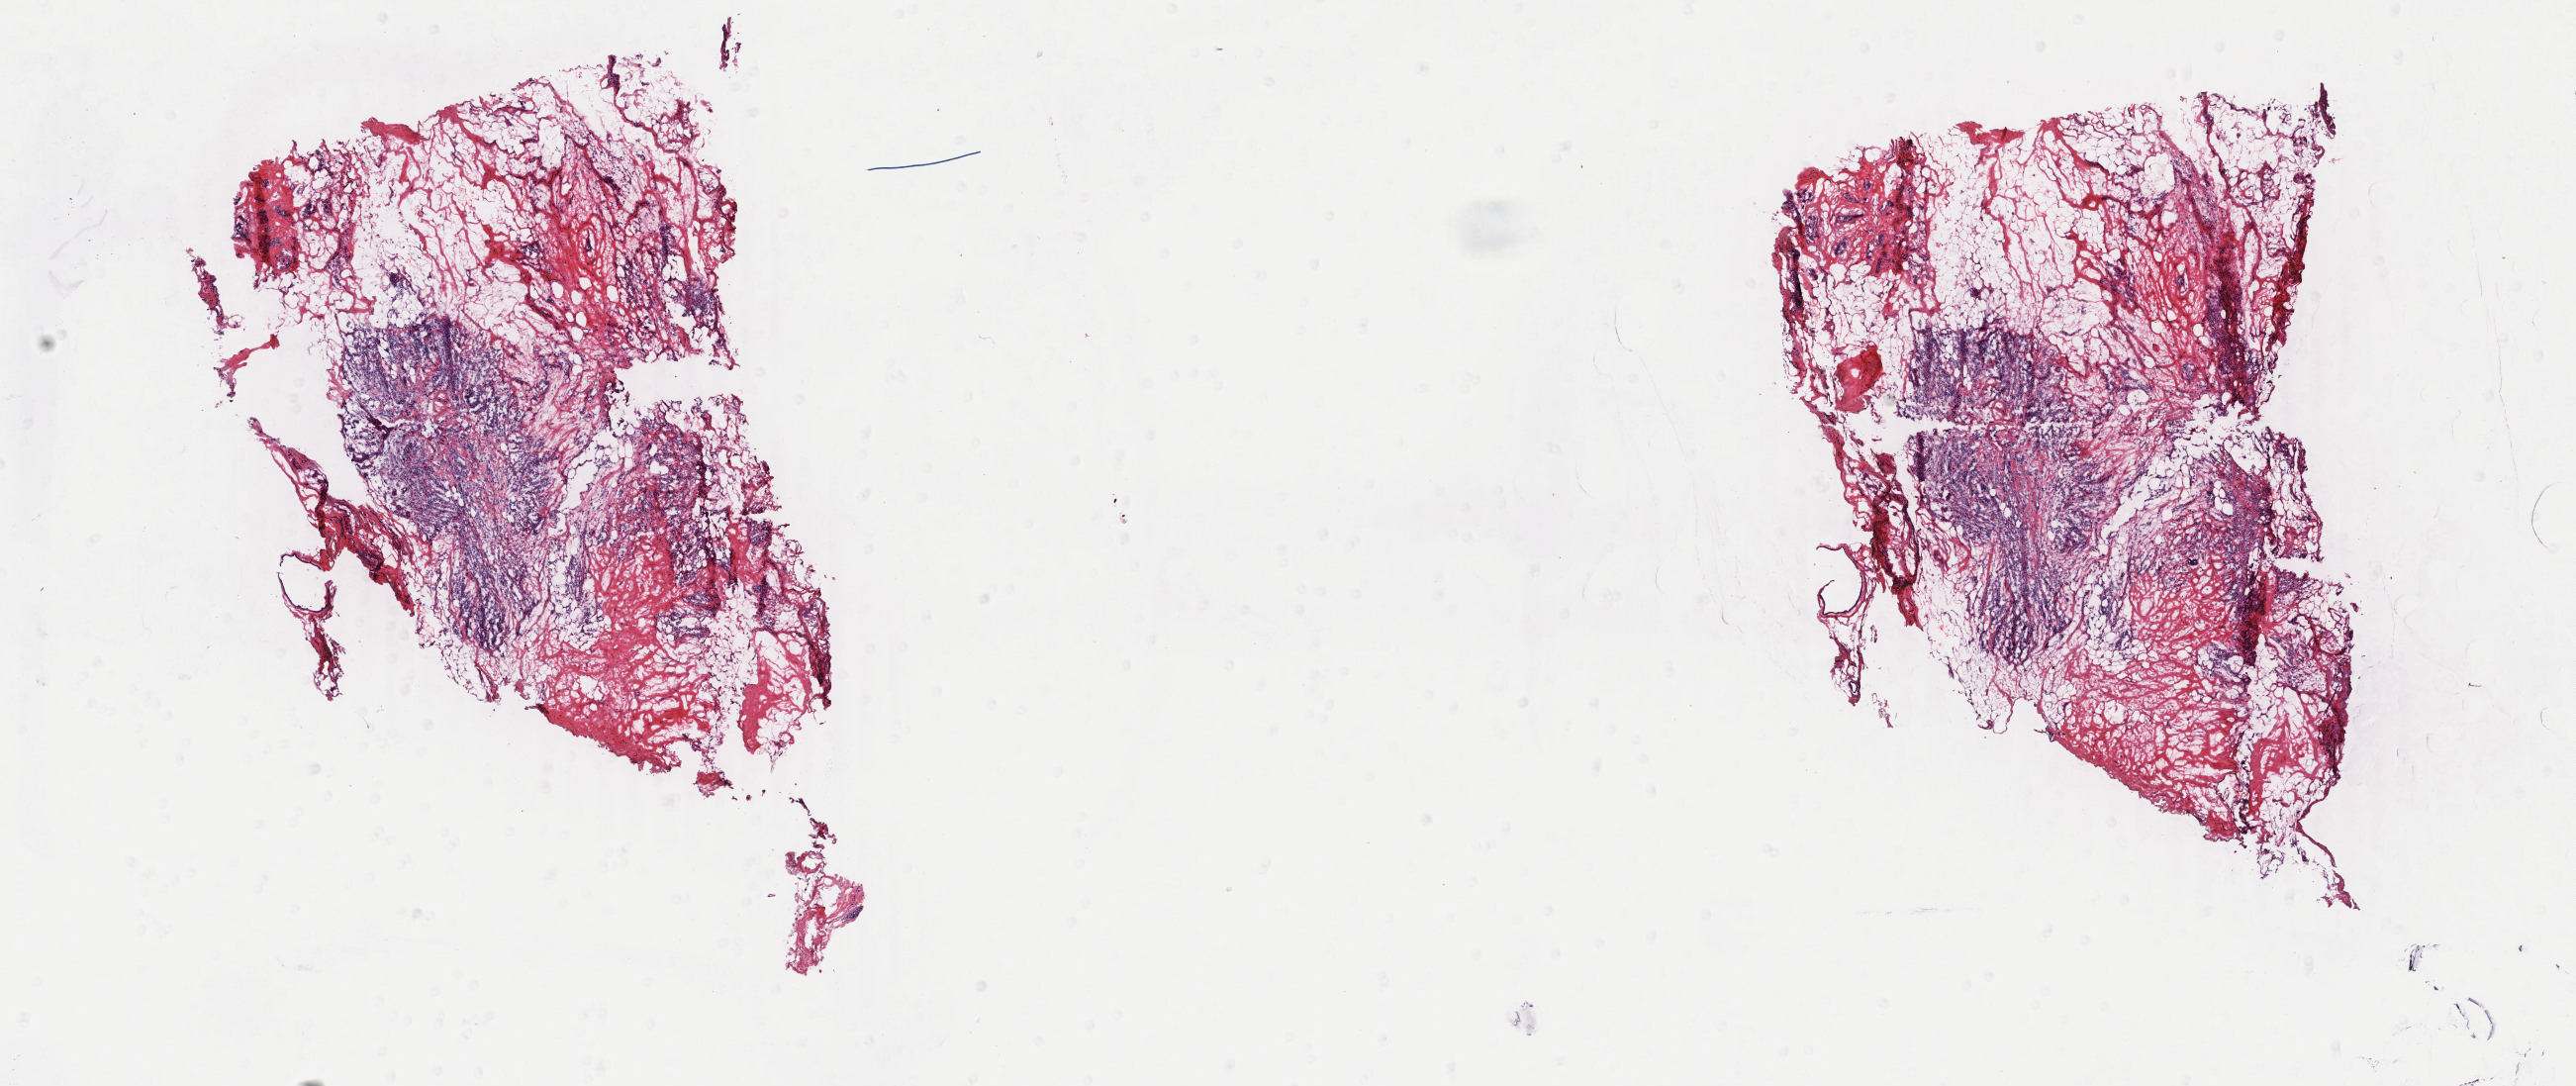
Hematoxylin and eosin (H&E) stained whole-slide image, whole scanned area (about 20.7 x 8.7 mm, acquisition: 40x scan) shown as a low-resolution overview; frozen section; breast, primary tumour sample. Patient sex: female. Slide review estimates, as recorded: tumour cells 30%, tumour nuclei 60%, normal cells 0%, stromal cells 70%, necrosis 0%. Inflammatory infiltration, as recorded: lymphocyte infiltration 0%, monocyte infiltration 0%, neutrophil infiltration 0%.
- AJCC pathologic stage: IIB (7th edition)
- histologic diagnosis: Lobular carcinoma, NOS
- laterality: right
- lymph nodes positive (case pathology): 0 of 11 examined